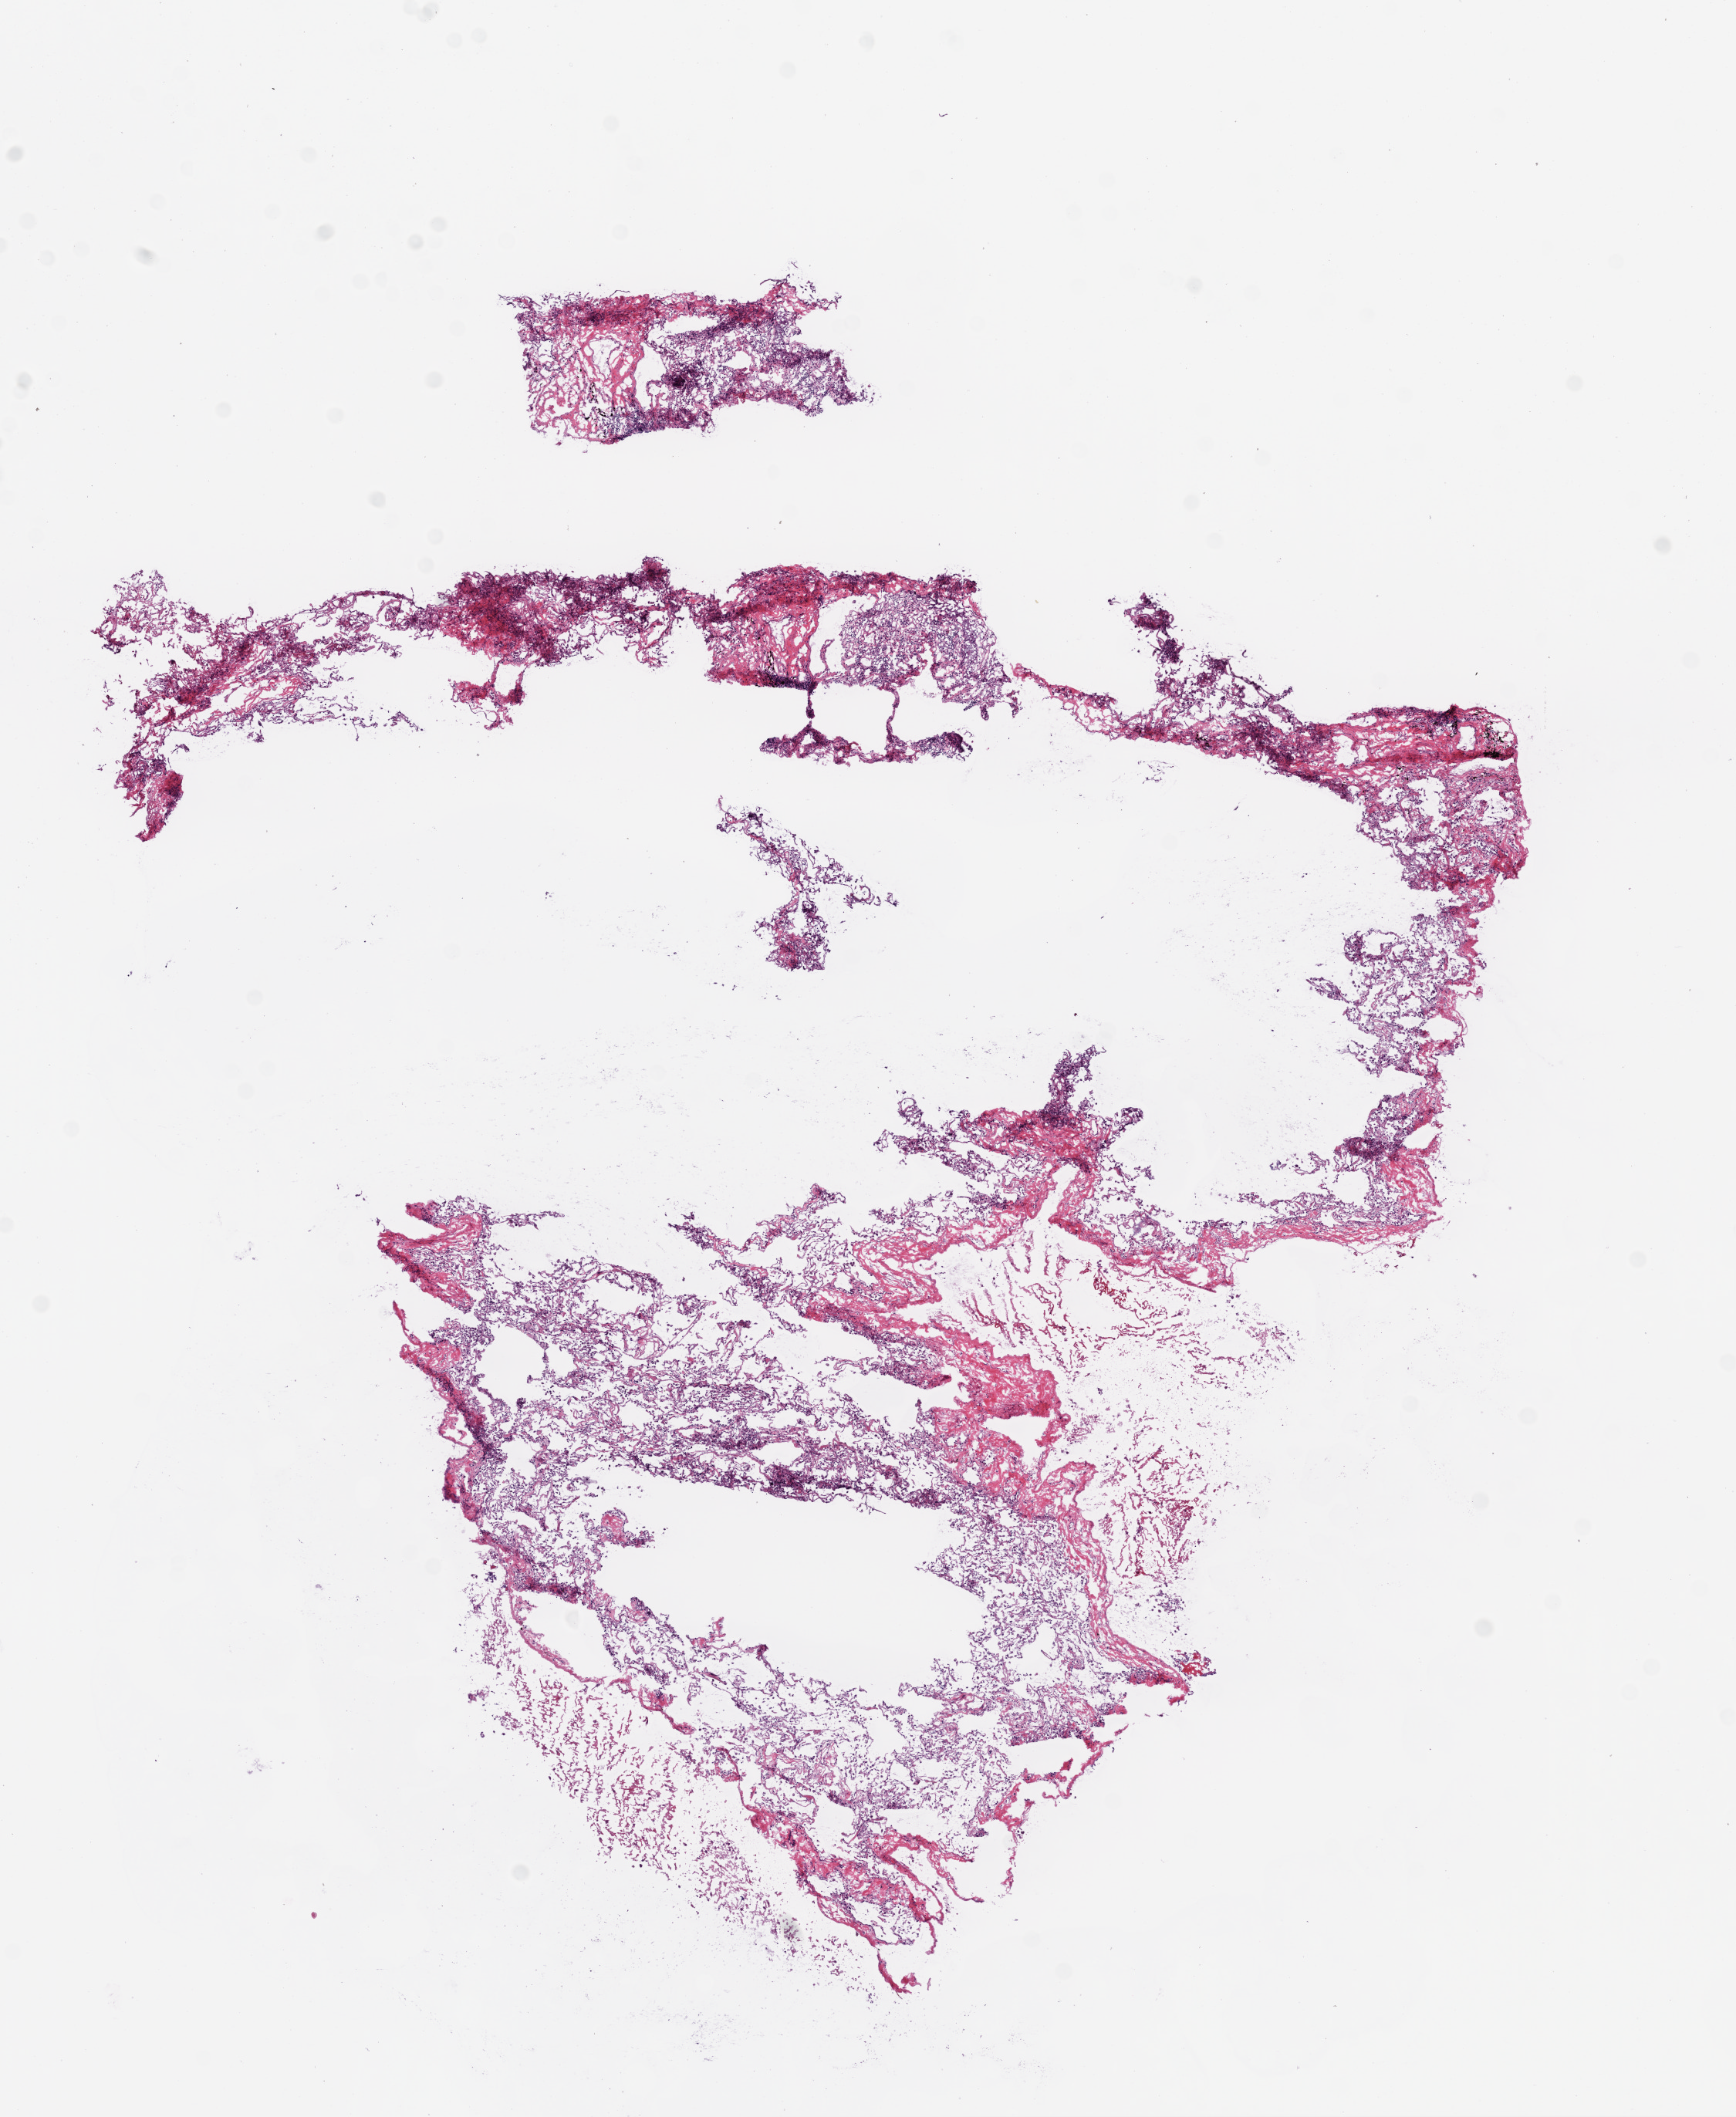
Hematoxylin and eosin (H&E) stained whole-slide image, a low-resolution overview of the entire scanned area, about 9.0 x 11.0 mm (acquisition: 20x scan), frozen section, solid tissue normal (non-tumour tissue) sample from the lung. Male, age 73 years at initial diagnosis.
• this section: solid tissue normal sample (biorepository sample class)
• patient diagnosis: Squamous cell carcinoma, NOS